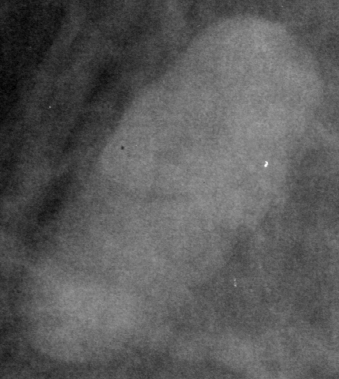
Crop from a digitized film mammogram around one marked abnormality, left breast, MLO view, BI-RADS breast density category 2 (scale 1–4).
Marked abnormality: mass, shape oval, margins circumscribed; BI-RADS assessment category 5; subtlety rating 5 on a 1 (subtle) to 5 (obvious) scale; pathology (as recorded): malignant.